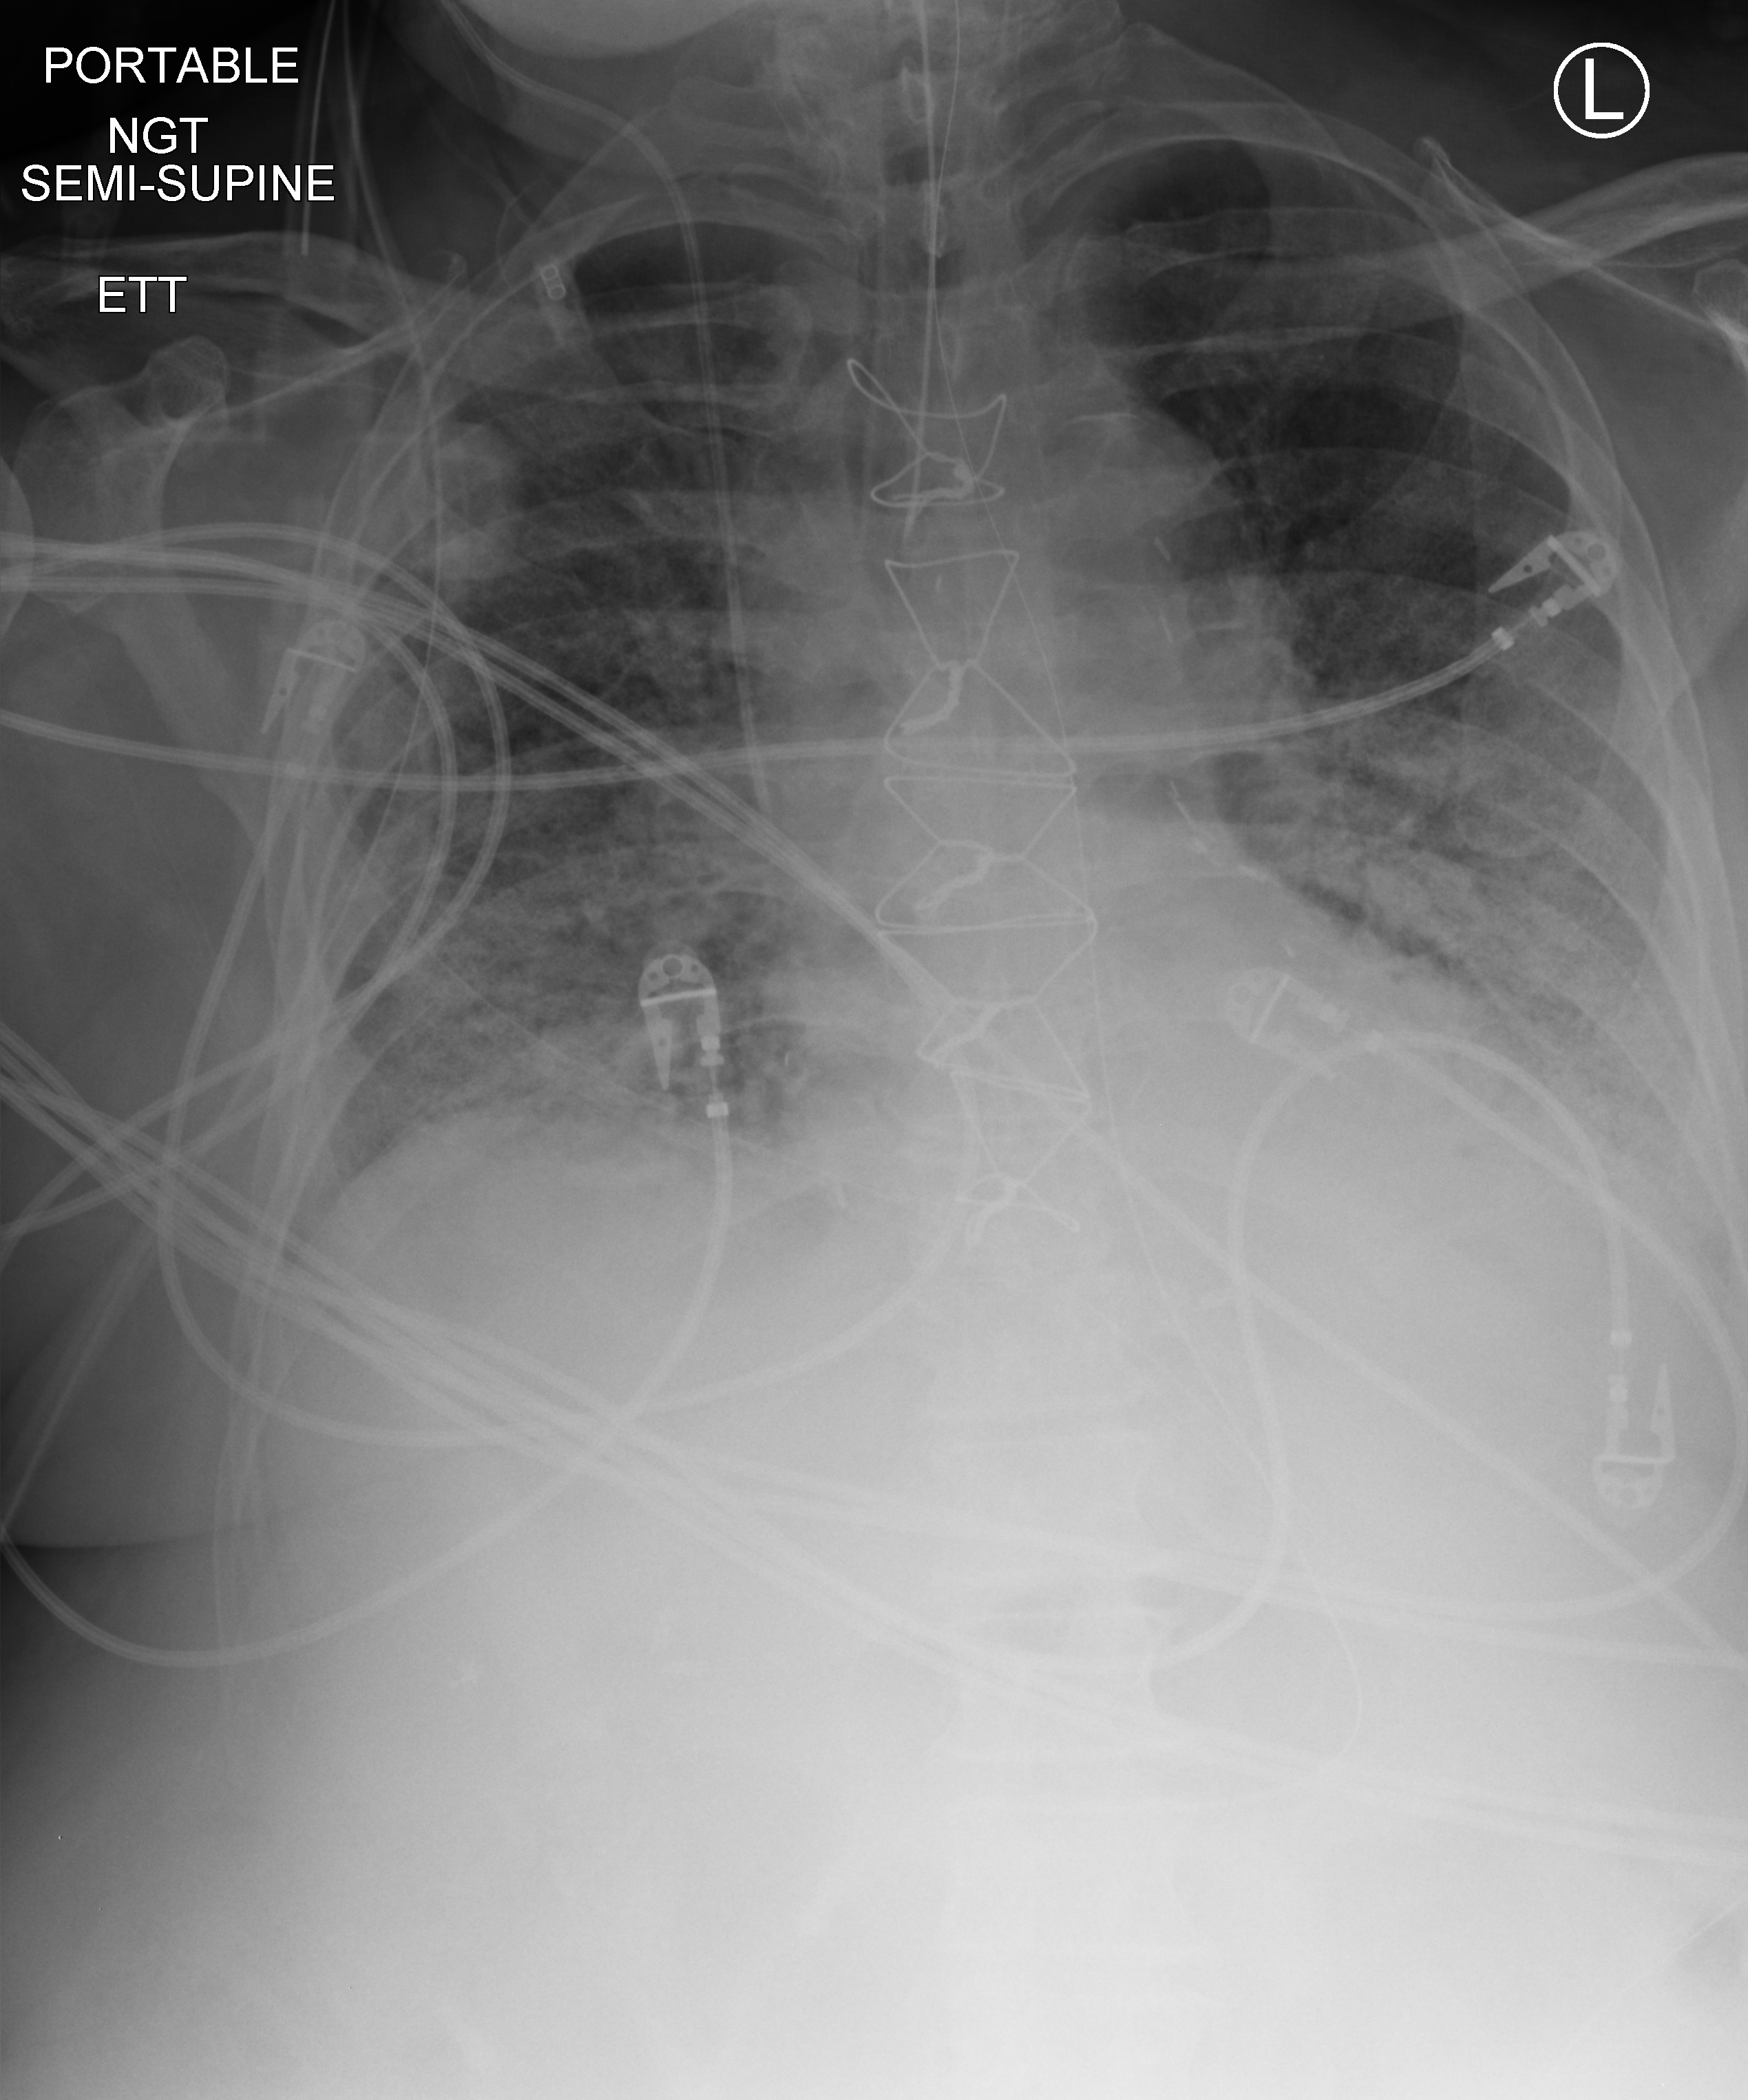
Portable chest radiograph; anteroposterior (AP) projection. Male patient hospitalised with COVID-19, age 75–90 years.
Admission-level facts for this patient (not findings on this image; timing relative to this image not recorded): diabetes (admission record): no; chronic kidney disease (admission record): no; mechanically ventilated during this hospital stay: yes.